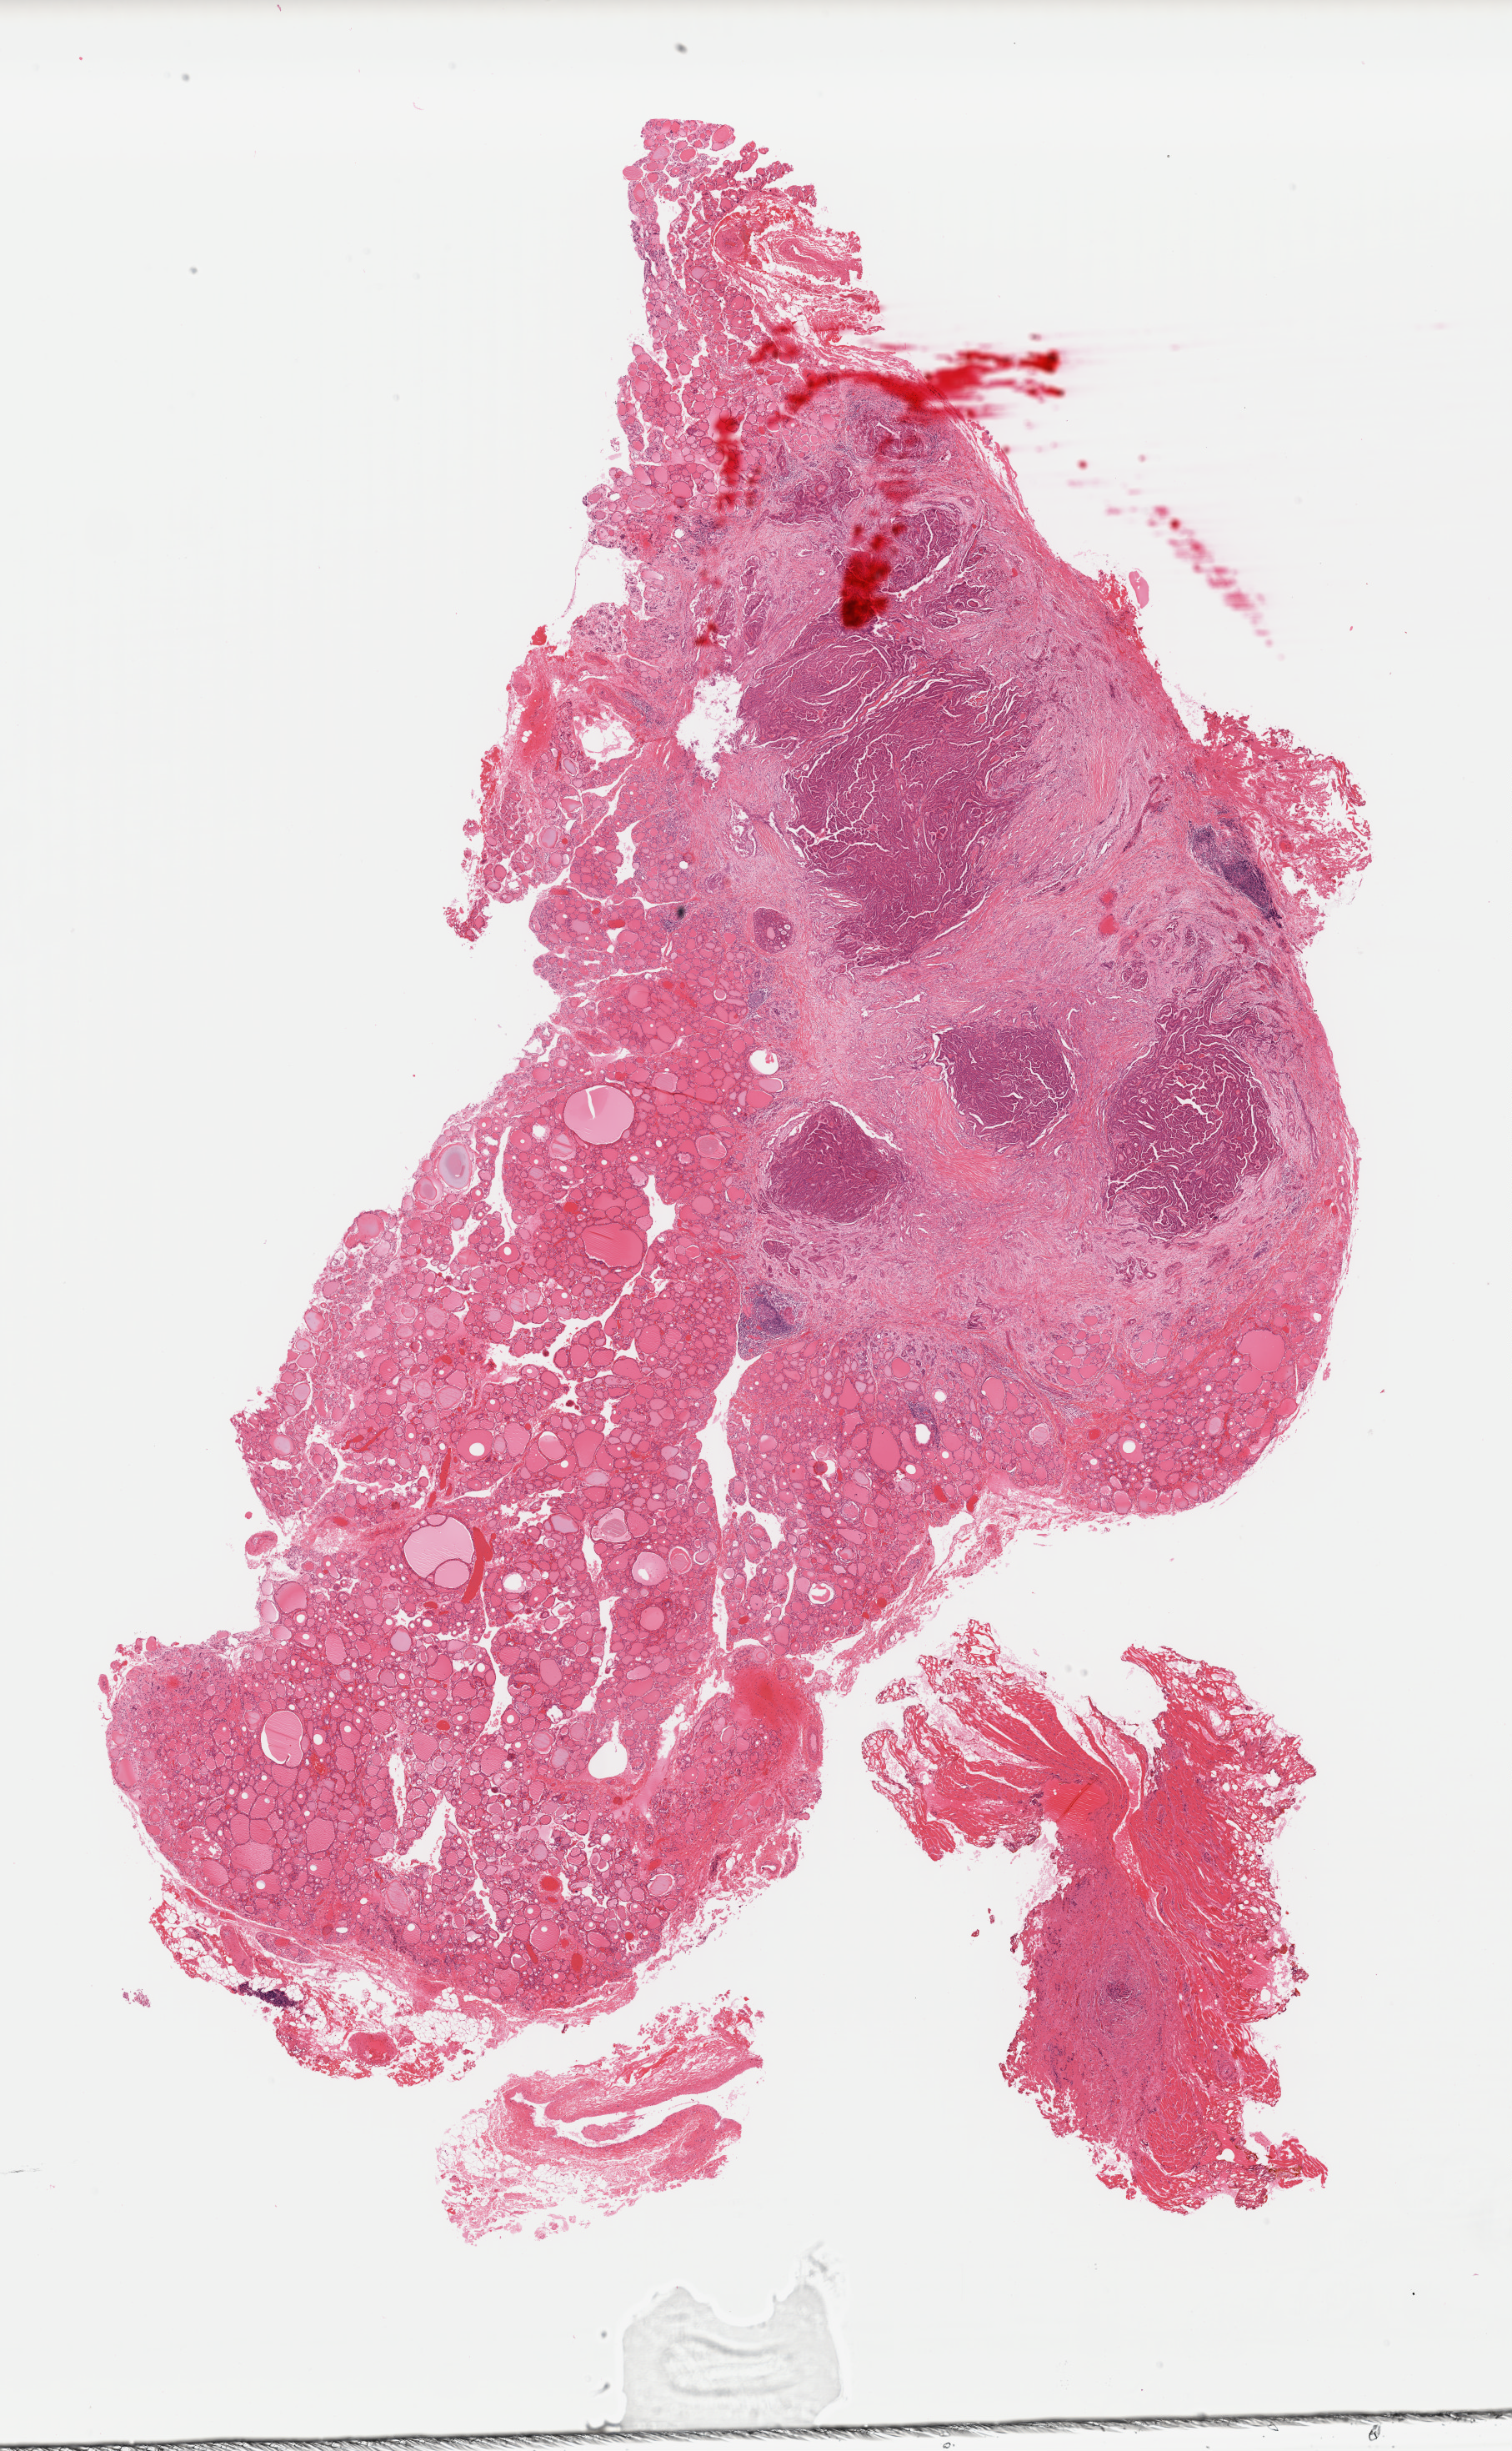
H&E-stained whole-slide image, whole scanned area (about 14.3 x 23.2 mm, slide scanned at 40x) shown as a low-resolution overview. Formalin-fixed paraffin-embedded (FFPE) diagnostic section. Thyroid, primary tumour sample. Patient: female, age at initial diagnosis 51 years.
* AJCC pathologic stage: I (7th edition)
* pathologic diagnosis: Papillary adenocarcinoma, NOS